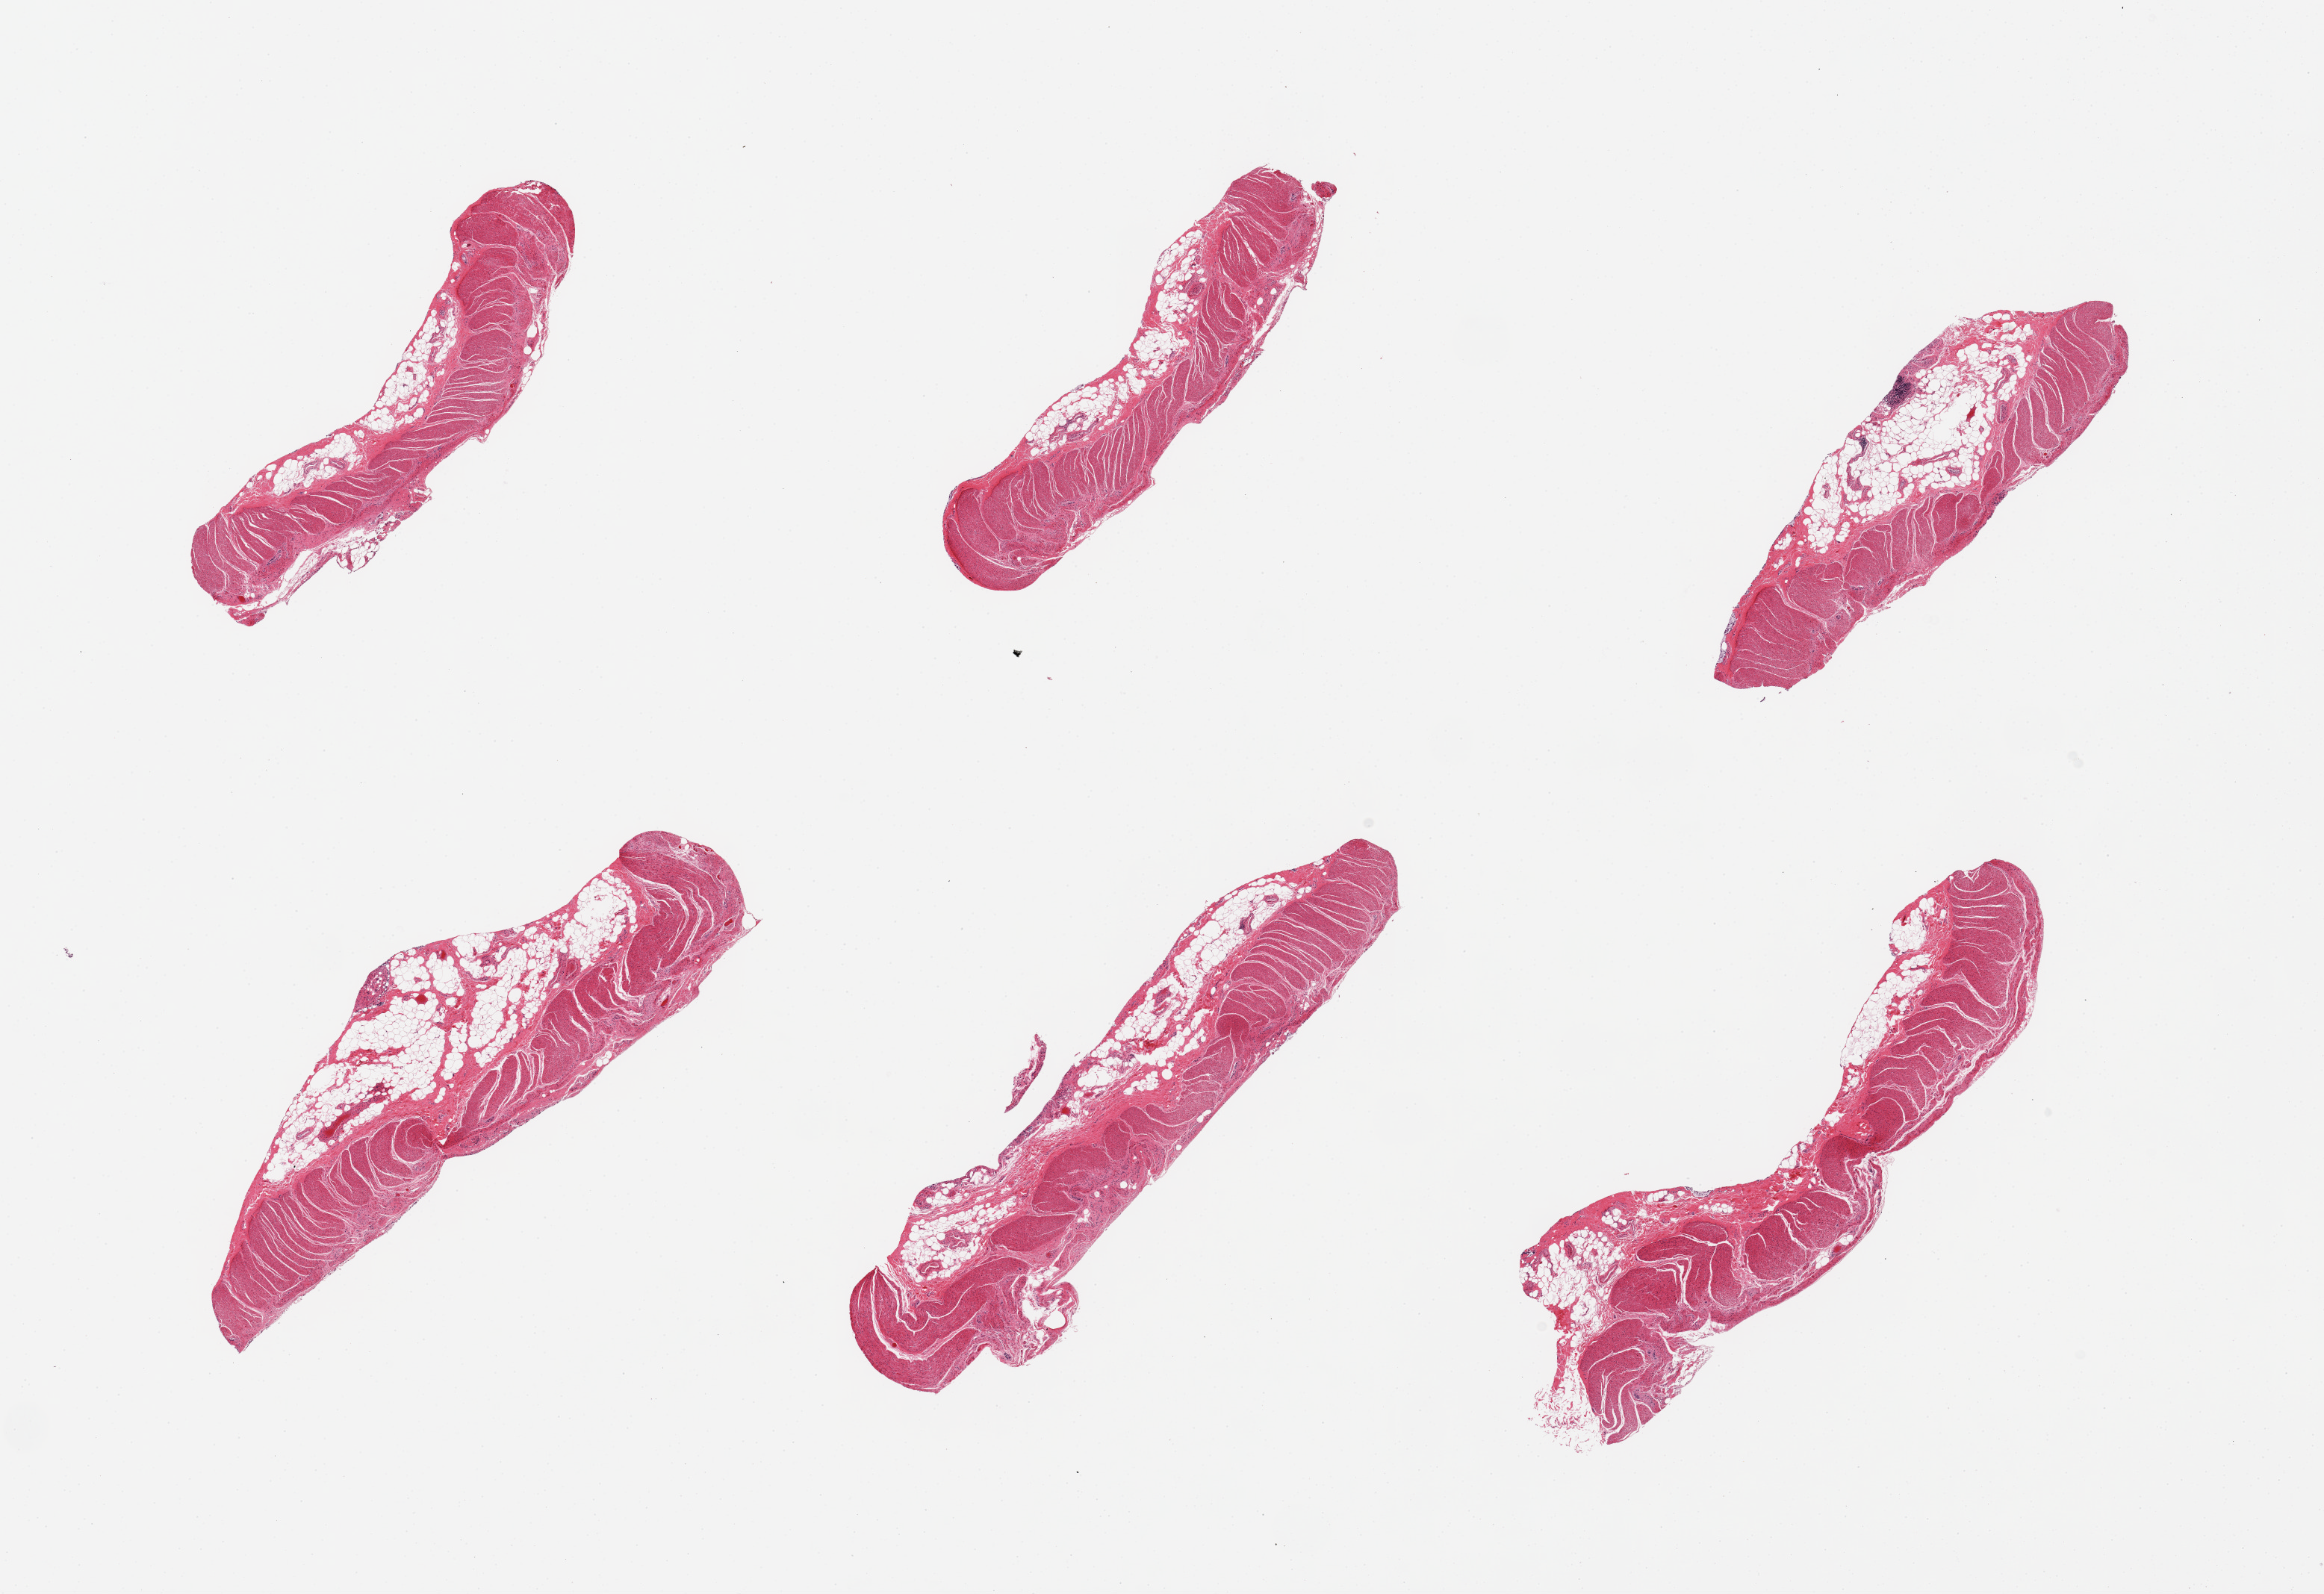
Digitized H&E-stained section, shown as a low-resolution overview of the whole scanned area (about 24.6 x 16.9 mm); PAXgene-fixed, paraffin-embedded tissue; sampled site (target tissue): sigmoid colon; donor tissue sample. Donor: male.
• review note (as recorded): 6 pieces; submucosal fat comprises up to 40%